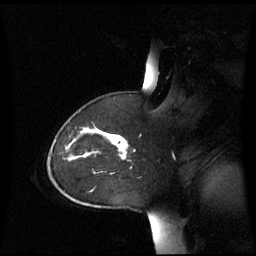
Breast MRI (dynamic contrast-enhanced), one sagittal slice. Position 45 of 60 along the scan axis. Dynamic contrast-enhanced series, image 2 of 3 at this slice position (ordered by acquisition). 1.5 T. TE 4.2 ms, TR 8.4 ms. 2.8 mm slice thickness. 256 × 256 image matrix. Patient: female, 43 years. Case-level facts recorded for this patient, not image findings: setting: breast cancer imaged before/during neoadjuvant chemotherapy; receptor status: triple-negative.
Outlined on this slice (semi-automatically segmented with operator editing):
- analysis volume of interest (the breast-tissue region the enhancement analysis was run in; not a lesion): box from (x=55, y=124) to (x=132, y=173) px
- tumour enhancement mask (voxels above the 70 % enhancement threshold inside the analysis volume of interest): (x=107, y=135)–(x=128, y=159)